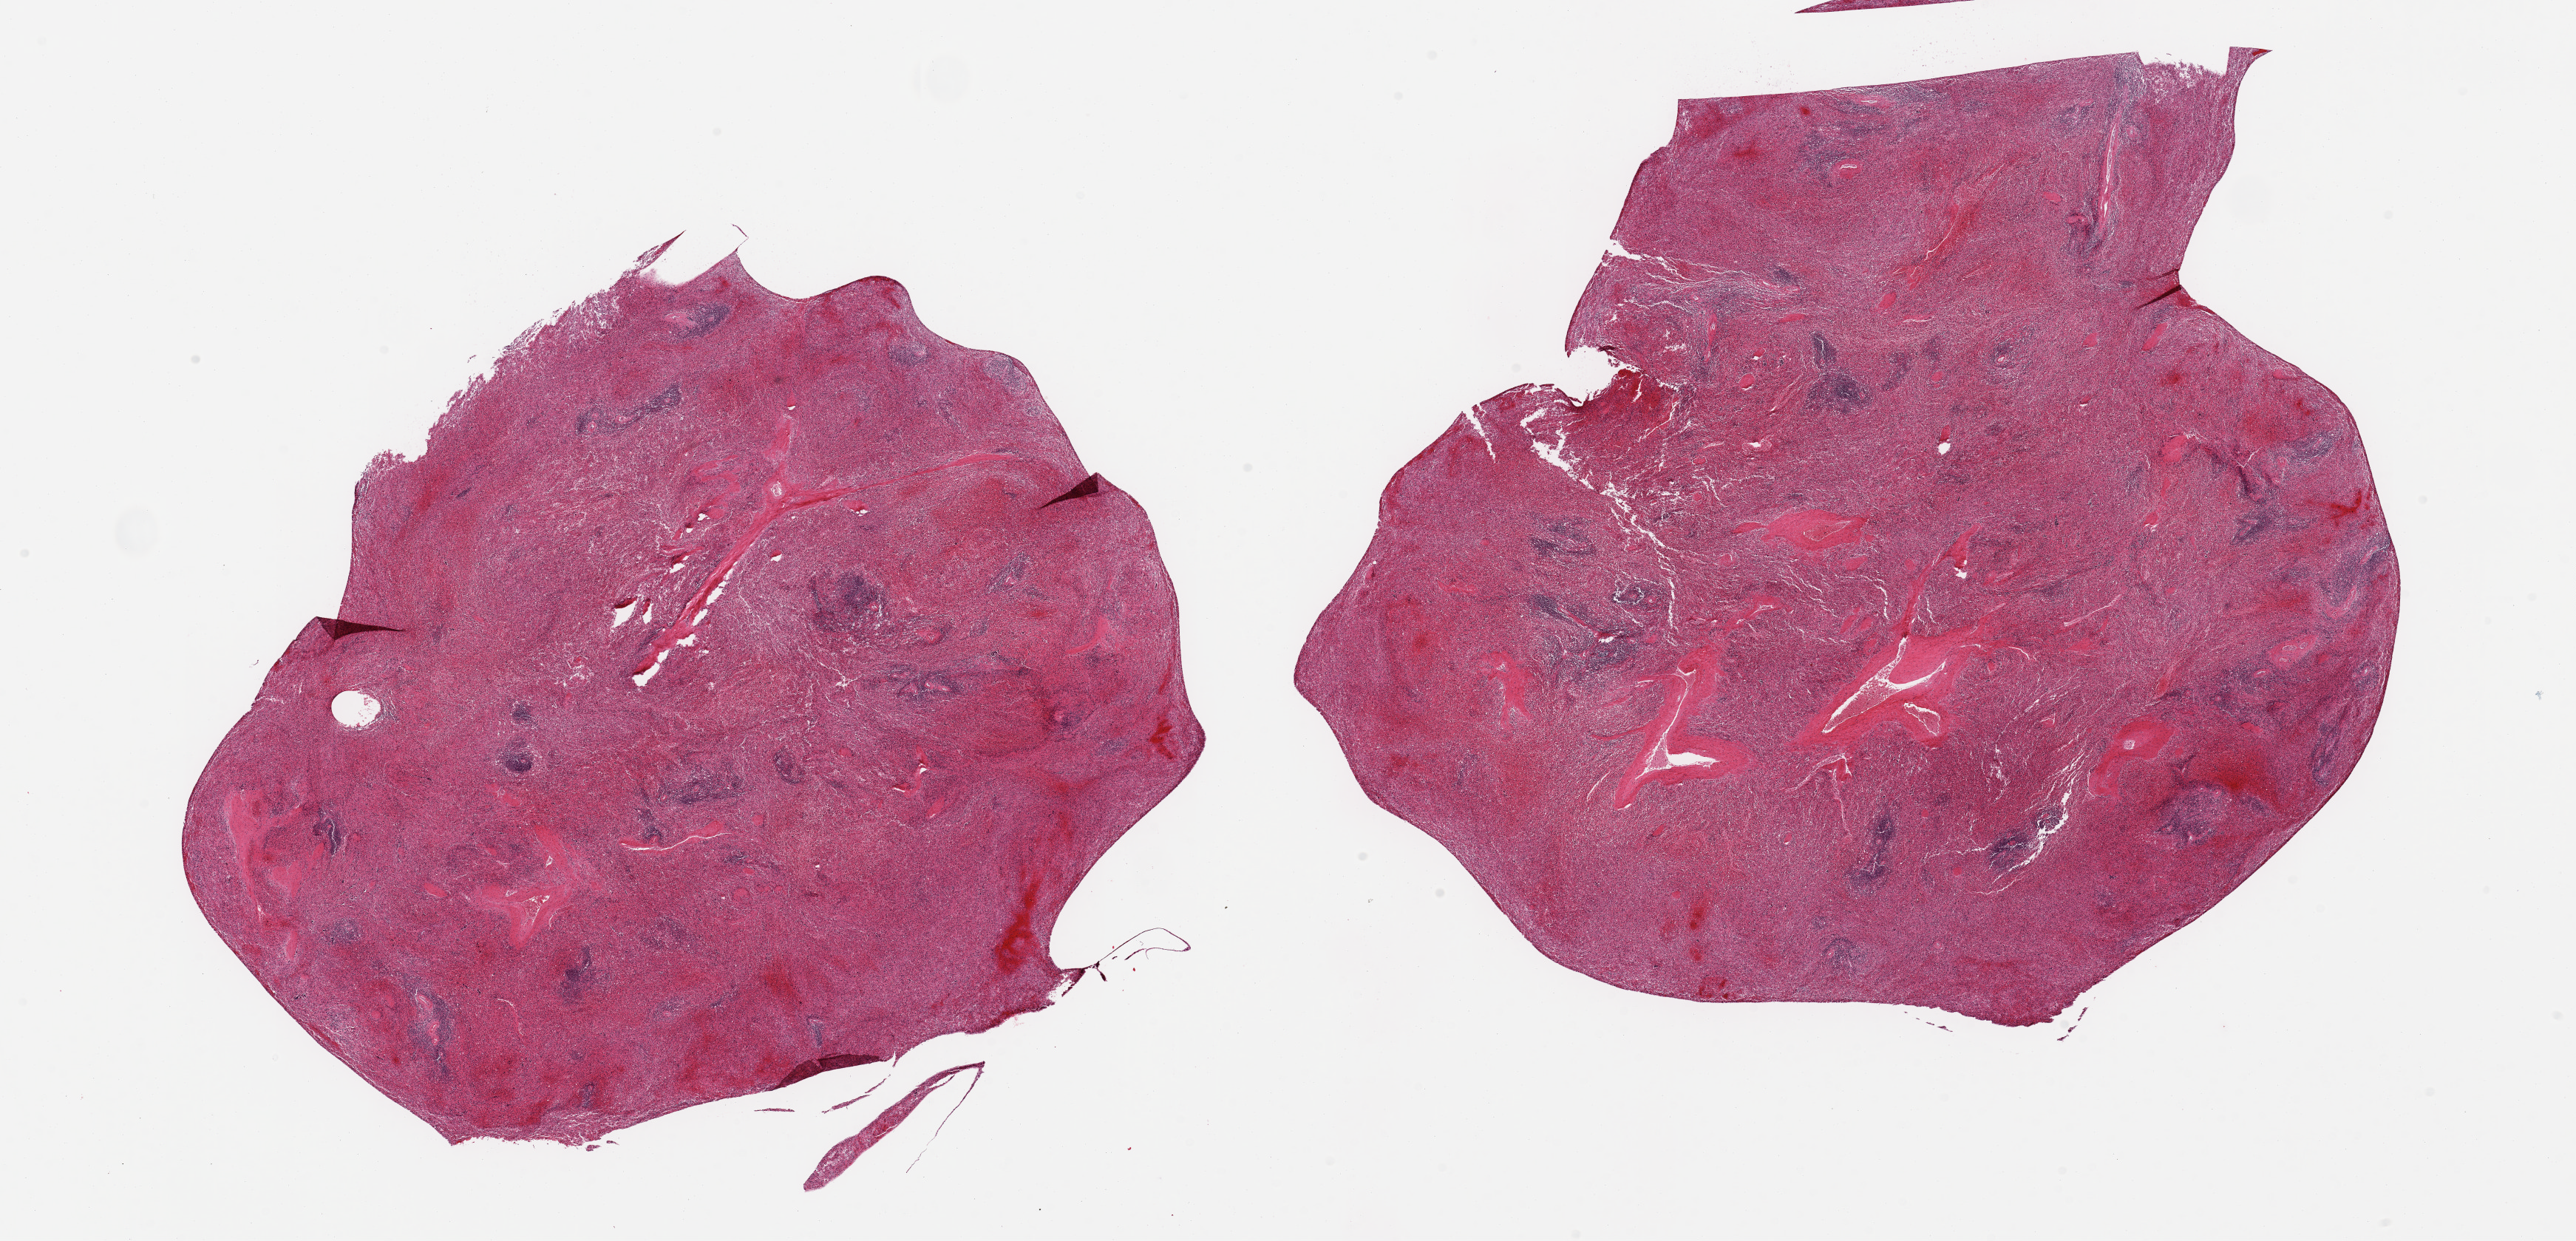
Haematoxylin and eosin whole-slide image, whole scanned area (about 27.6 x 13.3 mm) shown as a low-resolution overview; PAXgene-fixed, paraffin-embedded tissue; target tissue: spleen; tissue donor sample. Male donor.
Reviewer comment on this tissue sample: 2 pieces; marked congestion.